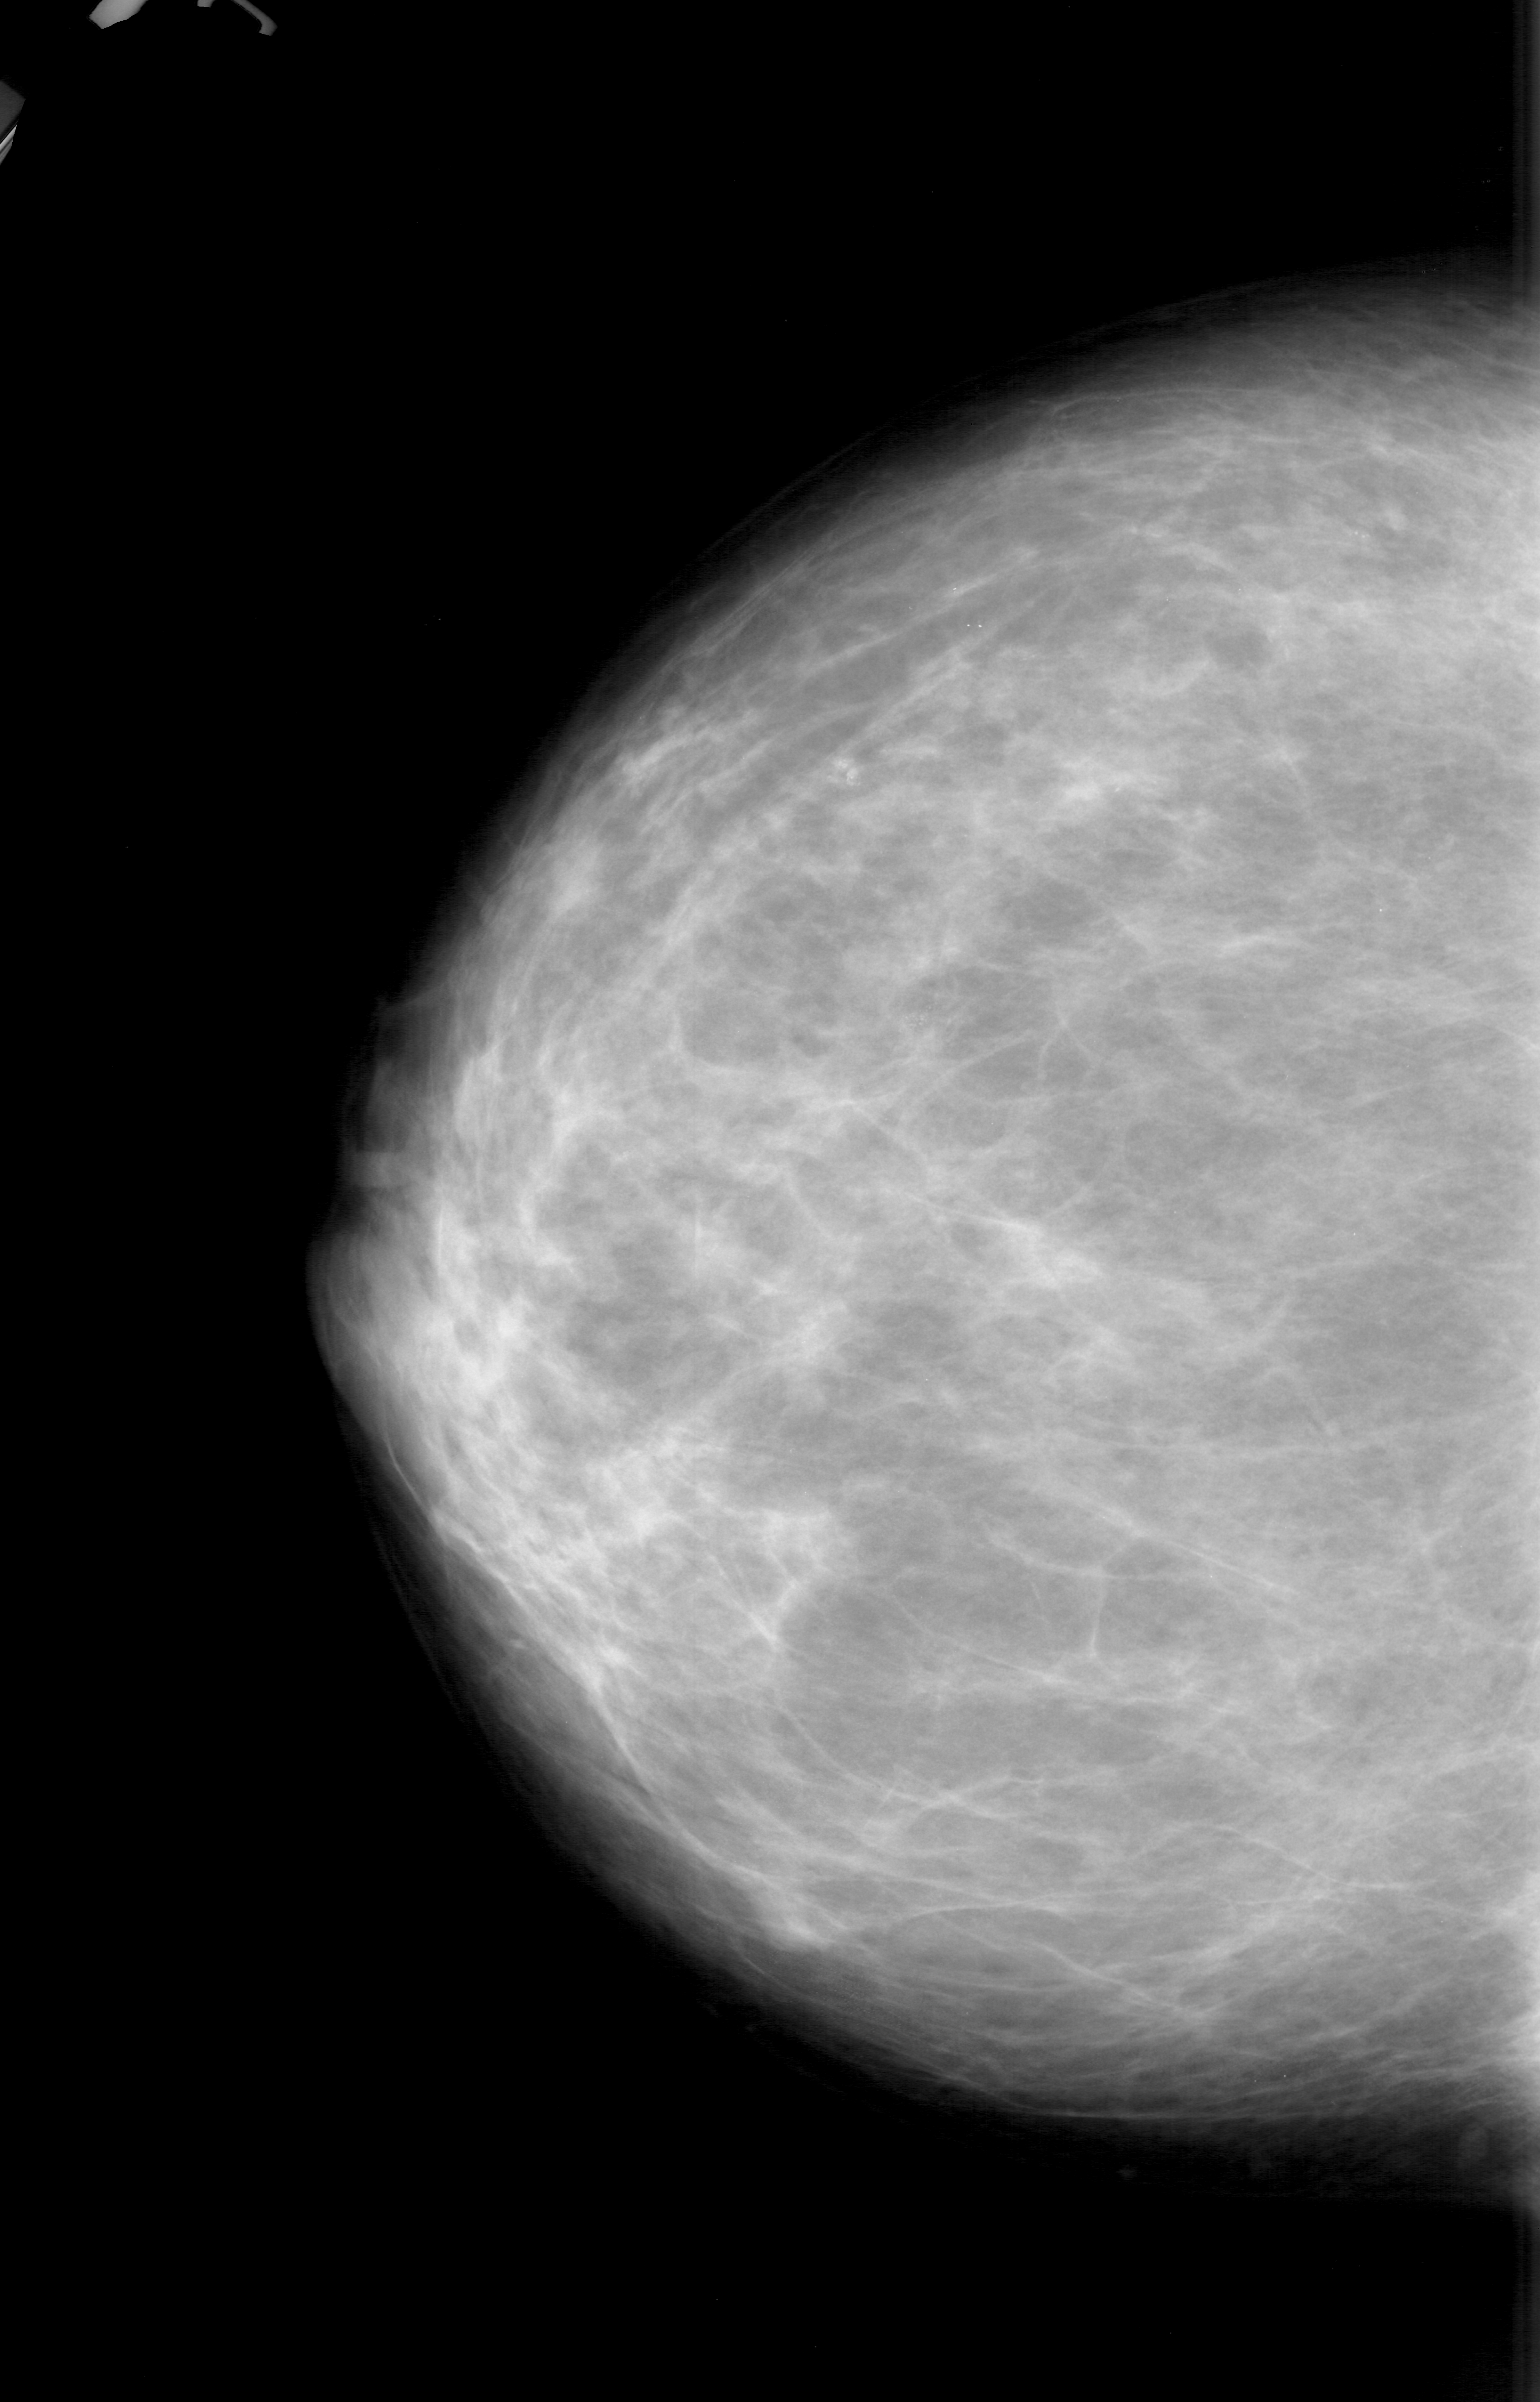
Digitized screen-film mammogram, left breast, CC view.
- Marked abnormality: calcifications, morphology pleomorphic, distribution clustered; BI-RADS assessment category 4; subtlety rating 2 on a 1 (subtle) to 5 (obvious) scale; pathology (as recorded): malignant.